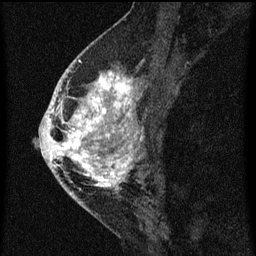
Breast MRI (dynamic contrast-enhanced), one sagittal slice. Position 28 of 60 along the scan axis. Dynamic contrast-enhanced series, image 2 of 3 at this slice position (ordered by acquisition). 1.5 T. TE 4.2 ms, TR 8 ms. 256 × 256 image matrix, field of view 180 × 180 mm. Female patient, age 46 years.
Annotated regions visible in this slice (semi-automatically segmented with operator editing):
- analysis volume of interest (the breast-tissue region the enhancement analysis was run in; not a lesion): bounding box [x1, y1, x2, y2] px = [48, 68, 138, 195]
- tumour enhancement mask (voxels above the 70 % enhancement threshold inside the analysis volume of interest): [48, 72, 138, 191]